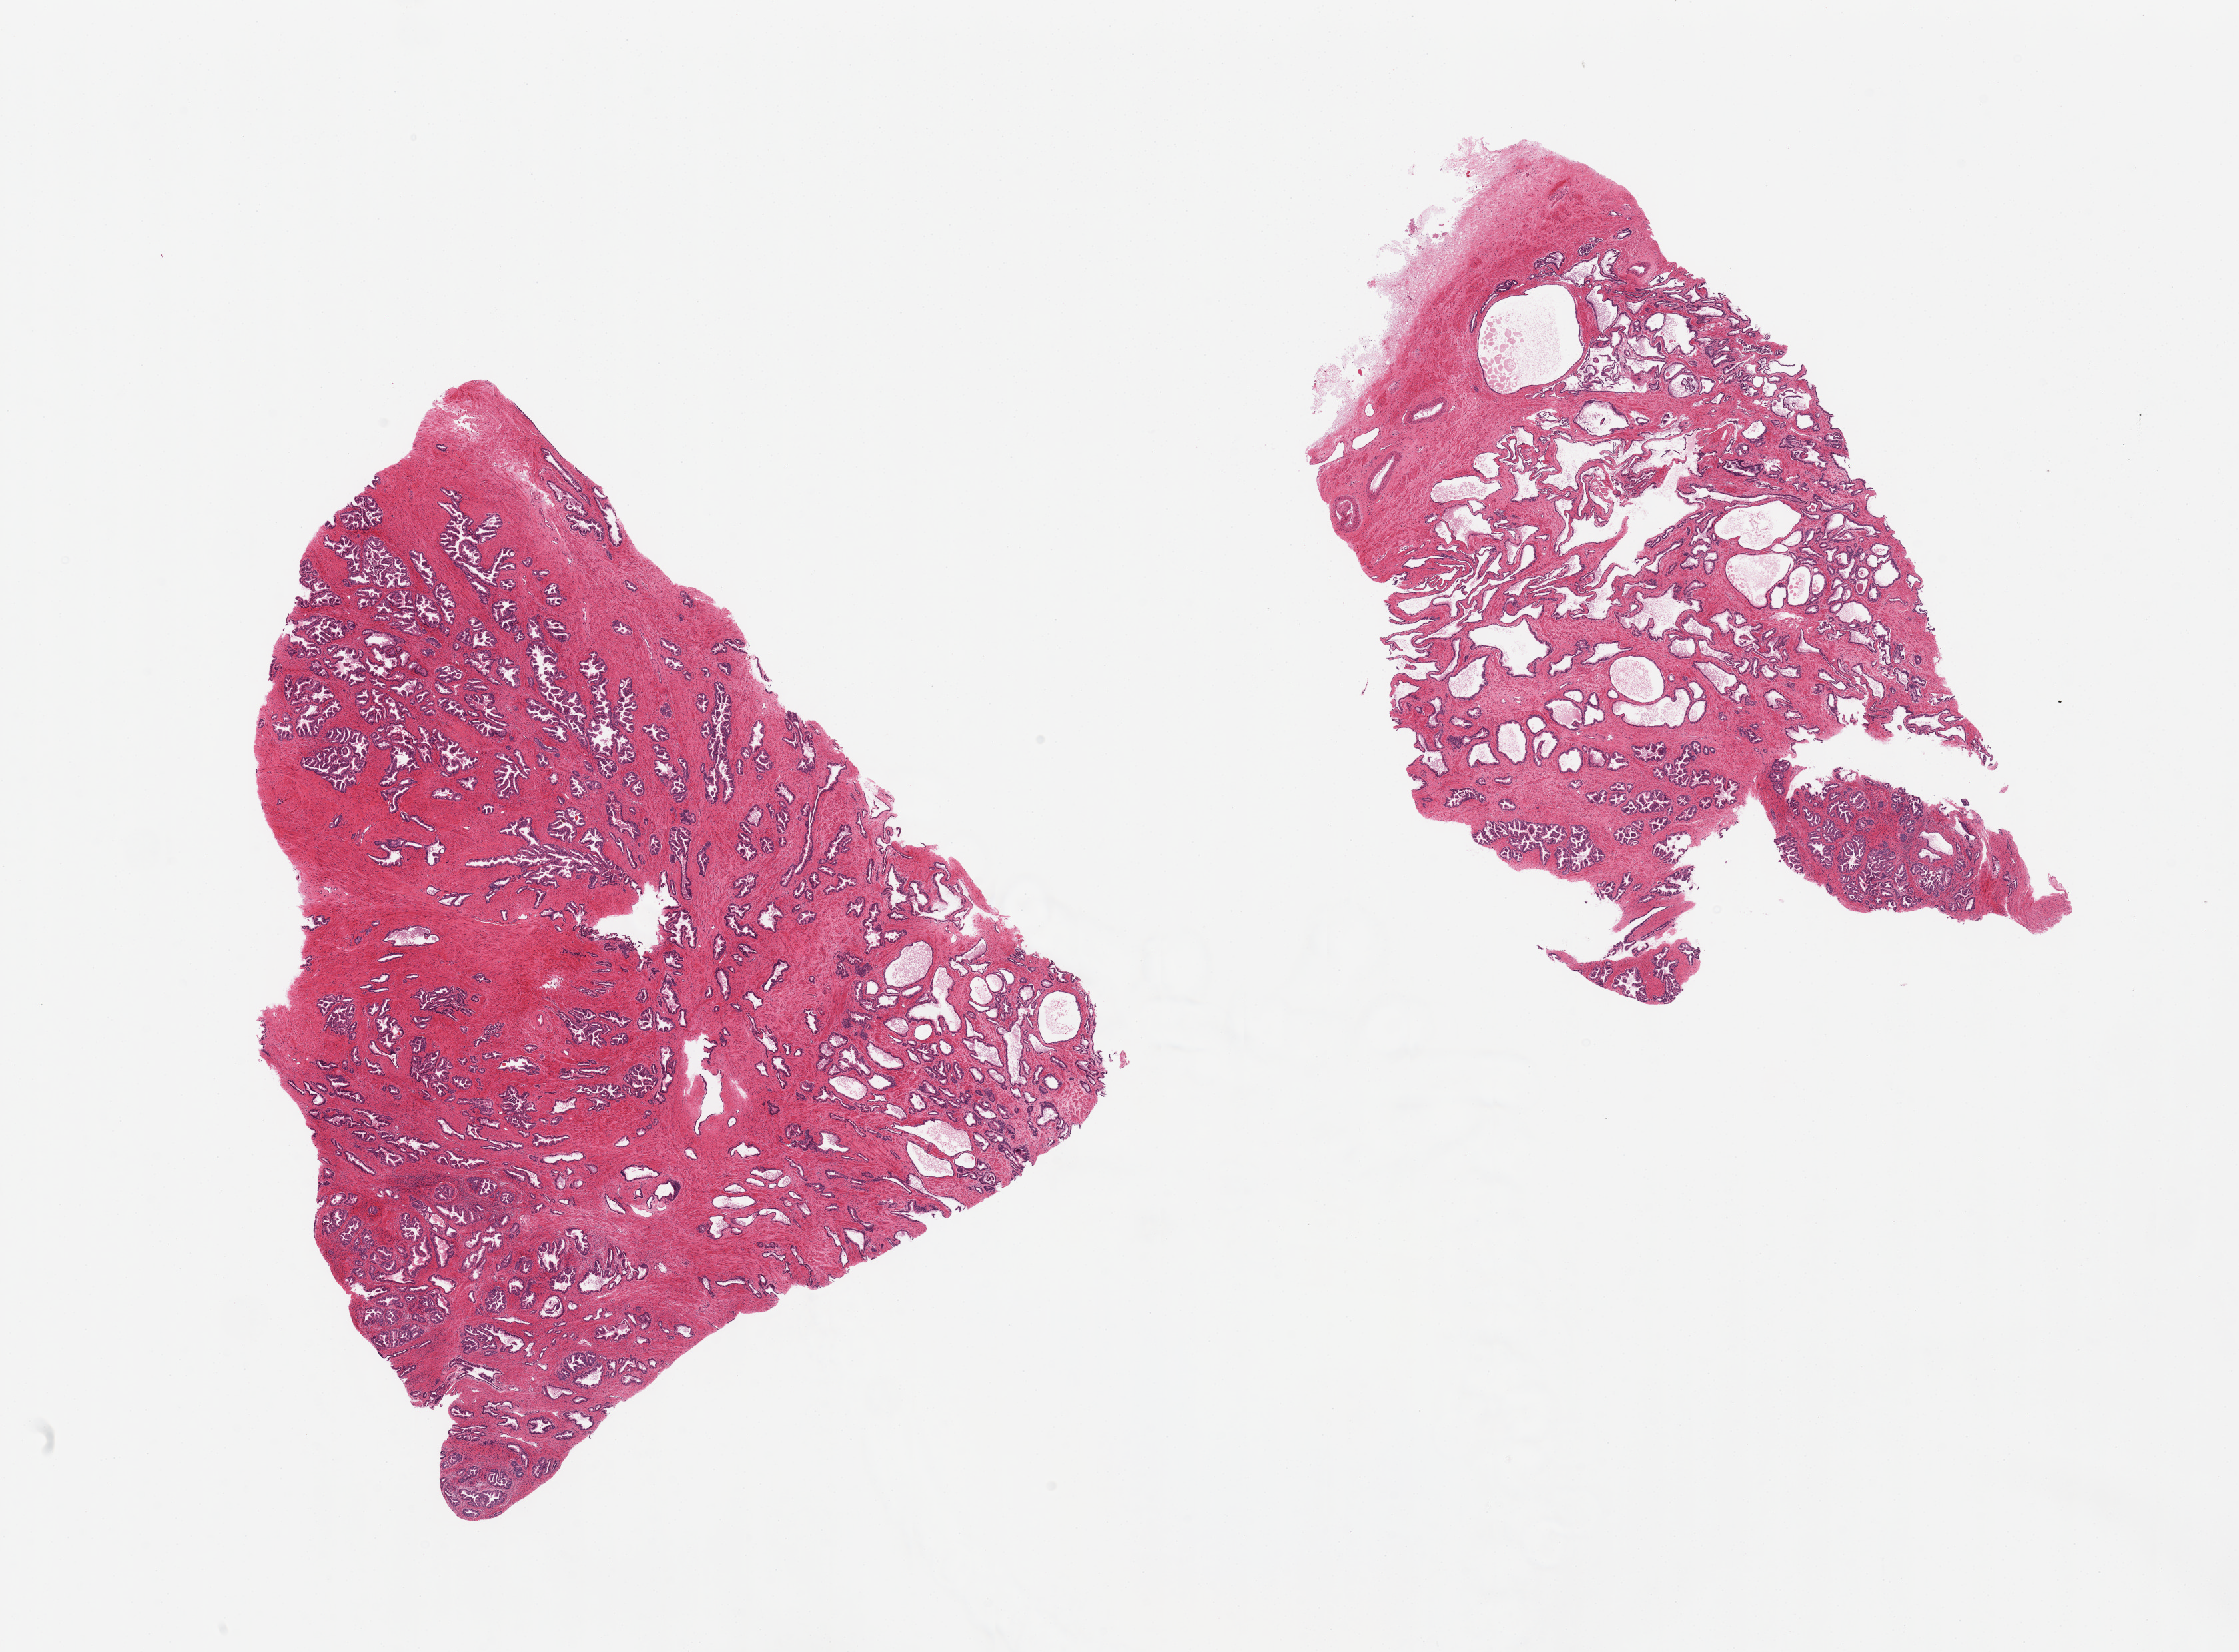
Digitized hematoxylin and eosin (H&E)-stained section, a low-resolution overview of the entire scanned area, about 26.6 x 19.6 mm (from a 20x scan). PAXgene-fixed, paraffin-embedded tissue. Section of prostate (target tissue). Tissue donor sample. Male donor.
Review note (as recorded): 2 pieces; glandular hyperplasia.